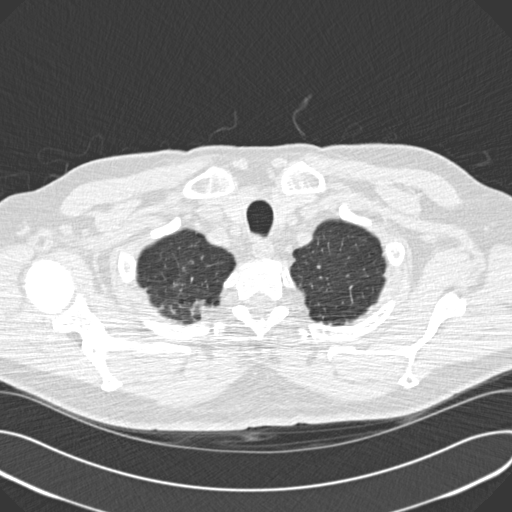
Low-dose screening chest CT, one axial slice. Position 163 of 180 along the scan axis. 120 kVp. Lung window (W 1500 / L -600 HU). 512 × 512 image matrix, field of view 376 × 376 mm.
Annotated regions visible in this slice (expert manual segmentation):
- lesion 1 (tumor, upper lobe of right lung): bounding box (x1, y1, x2, y2) in pixels: (198, 302, 214, 318)